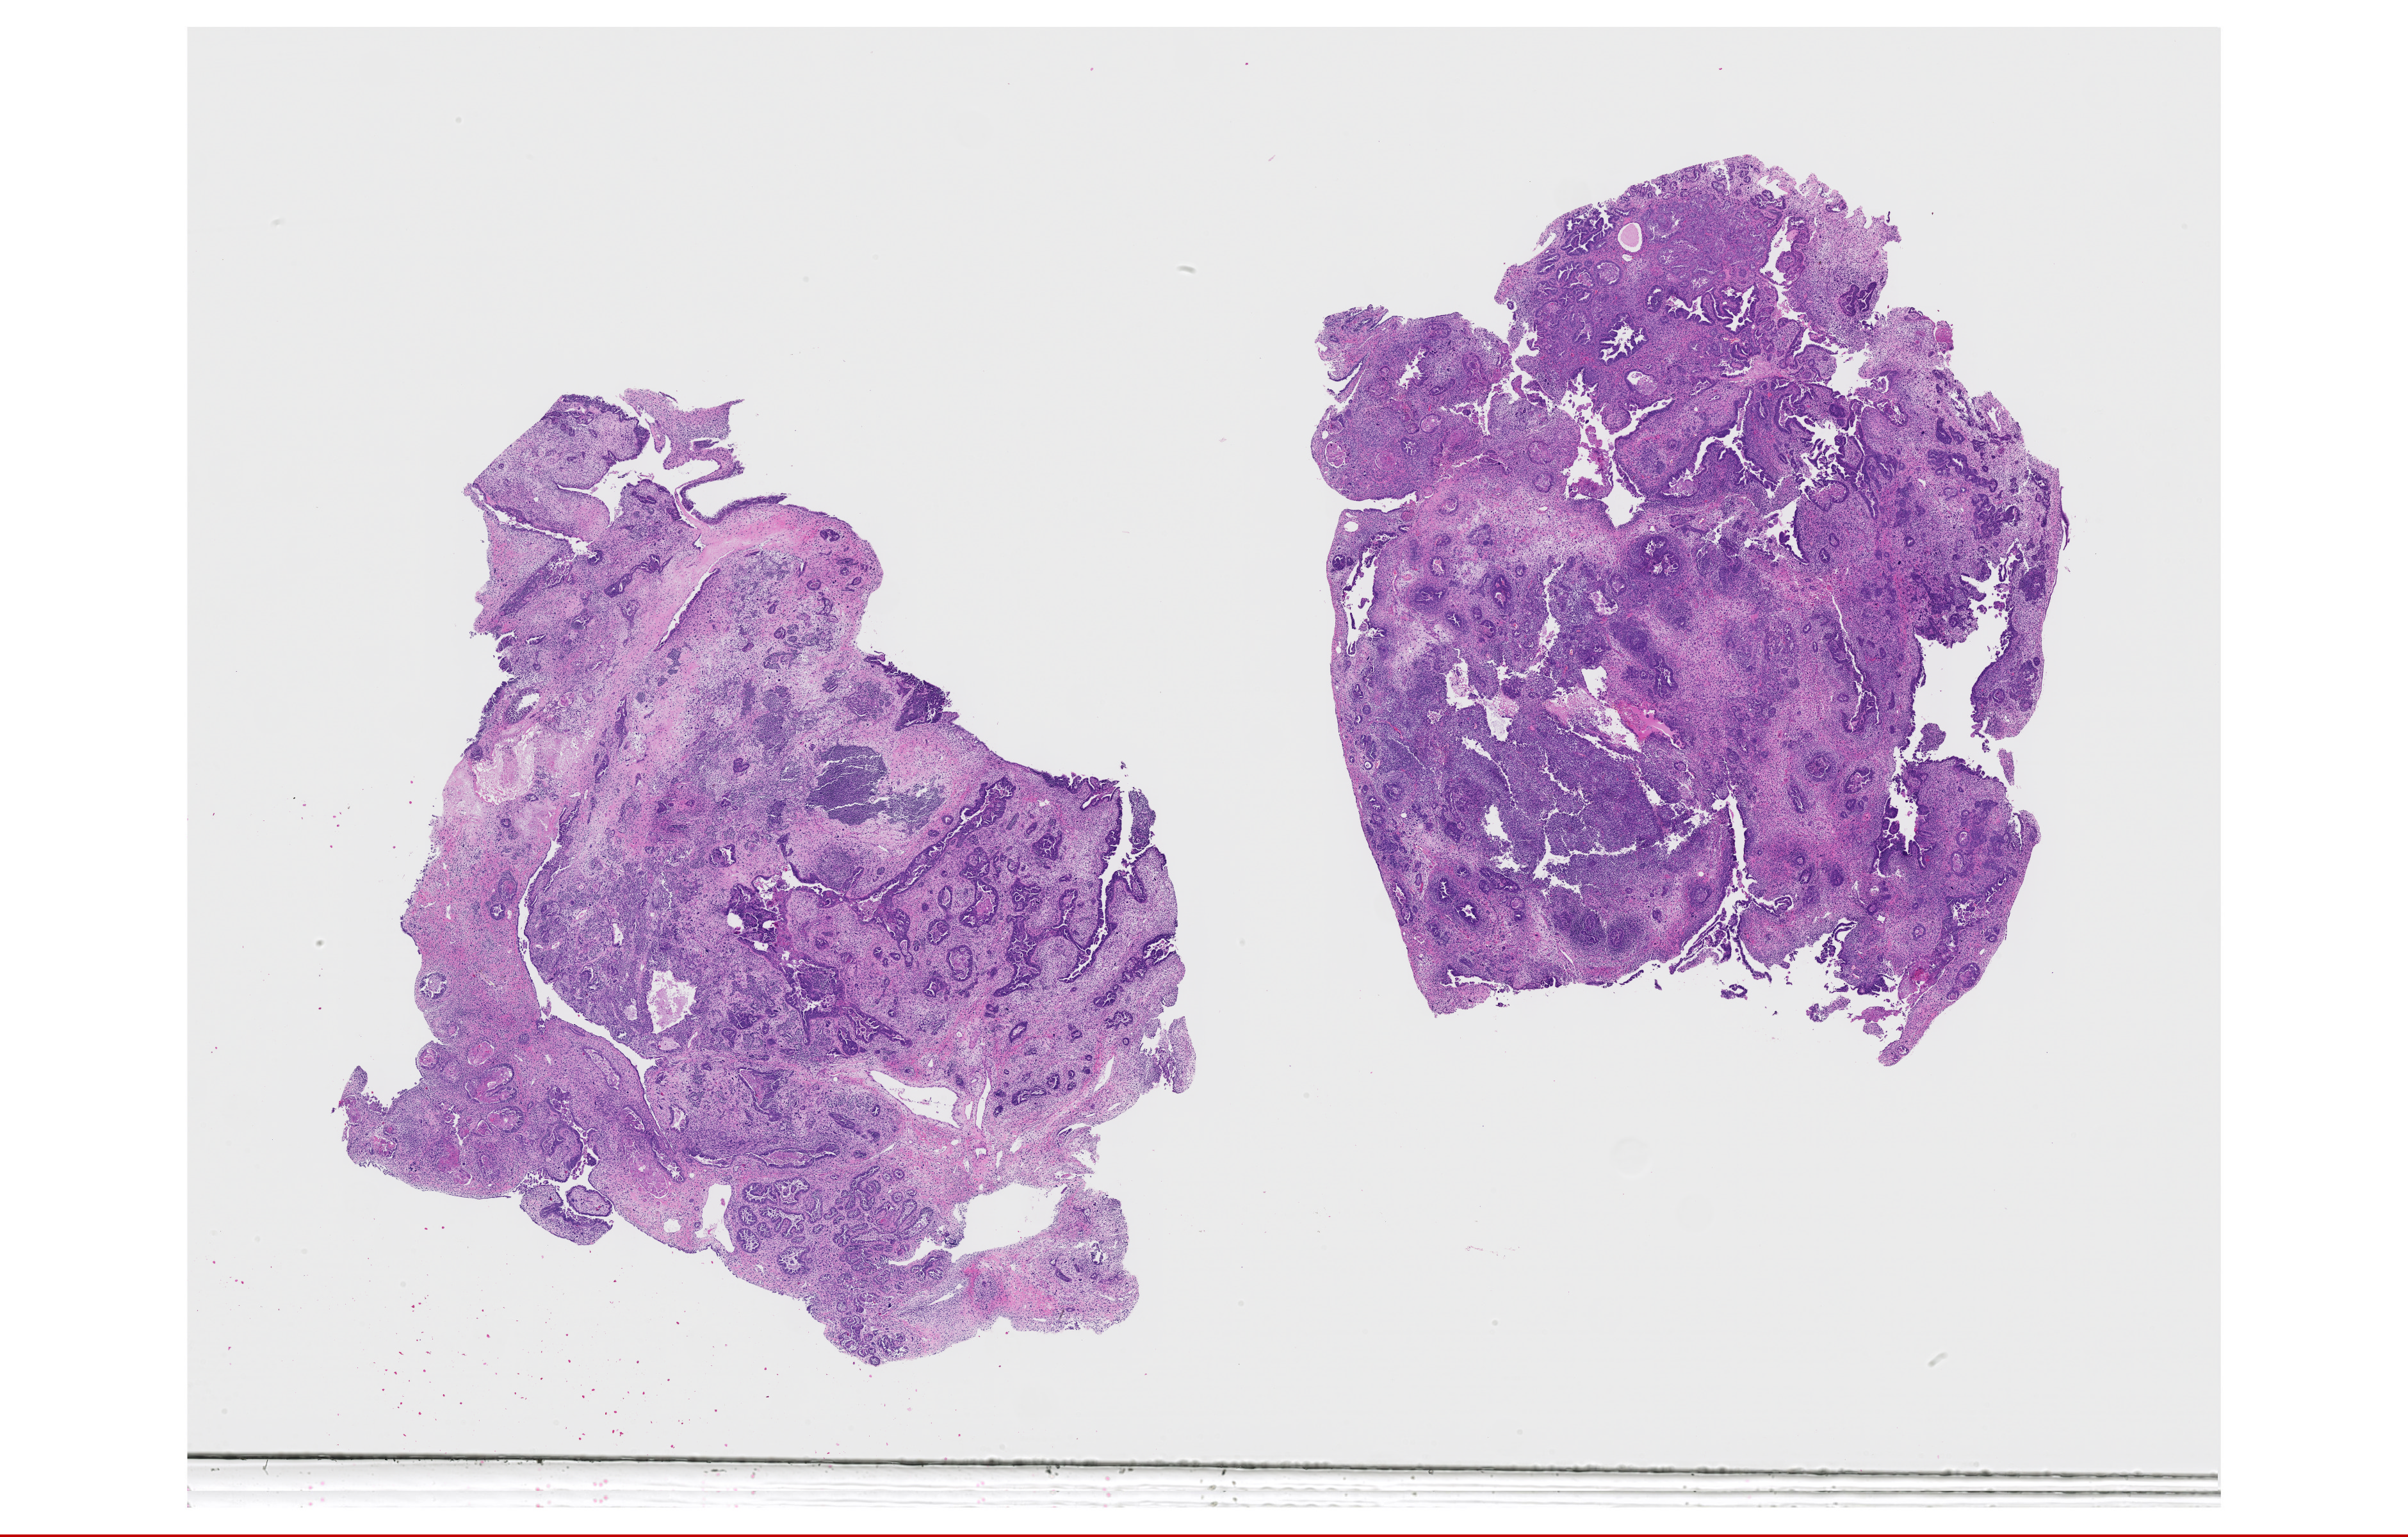
H&E whole-slide image, low-resolution overview of the scanned area, about 30.1 x 19.2 mm (acquisition: 20x scan). FFPE section. Primary tumour sample from the uterus. Patient: female, age at initial diagnosis 61 years.
FIGO stage: IV. Pathologic diagnosis: Mullerian mixed tumor.